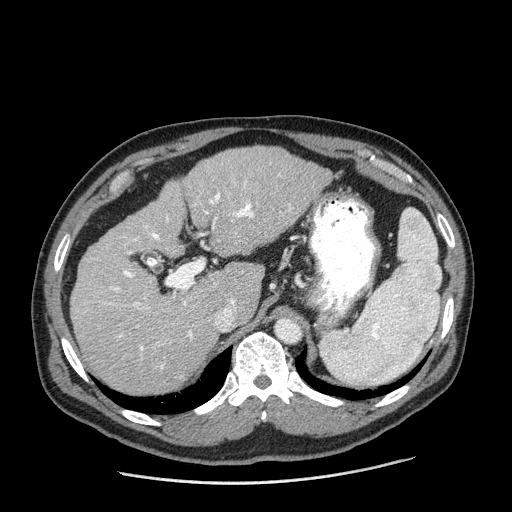
Contrast-enhanced abdominal CT (liver protocol), one axial slice. Slice 125 of 198 in the series (ordered by position). 120 kVp. One of 2 acquisitions stored at this slice position. Soft-tissue window (W 400 / L 40 HU). 512 × 512 image matrix. Case-level facts recorded for this patient, not image findings: diagnosis: hepatocellular carcinoma (patient treated with transarterial chemoembolisation; whether this scan precedes or follows treatment is not stated here); TNM stage (as recorded): Stage-II; Child-Pugh class: A; tumour differentiation: moderately differentiated; tumour size: 2.6 cm.
Annotated regions visible in this slice (semi-automatic segmentation, software-assisted and operator-edited):
- liver parenchyma outside the tumour (the mass and vessels are separate outlines, so this box may not span the whole liver): box from (x=70, y=146) to (x=332, y=392) px
- liver vessels: (x=108, y=174)–(x=291, y=369)